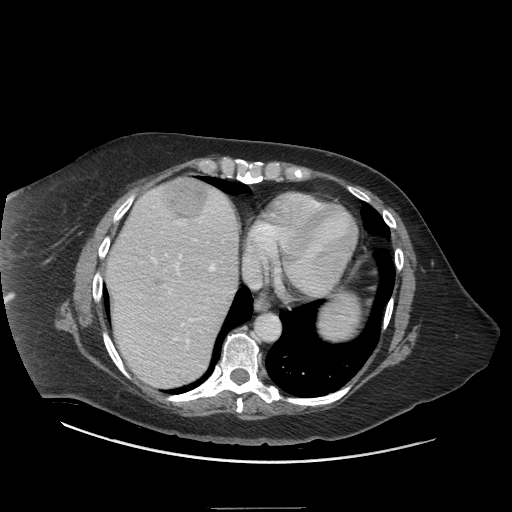
Contrast-enhanced abdominal CT (liver protocol), one axial slice; slice 60 of 81 in the series (ordered by position); soft-tissue window (W 400 / L 40 HU); 512 × 512 image matrix. From the clinical record (not read from this slice): diagnosis: hepatocellular carcinoma (patient treated with transarterial chemoembolisation; whether this scan precedes or follows treatment is not stated here); TNM stage (as recorded): Stage-II; Child-Pugh class: A; tumour nodularity: multinodular; tumour size: 1.7 cm.
Outlined on this slice (semi-automatic segmentation, software-assisted and operator-edited):
- abdominal aorta: bounding box <256,314,279,341> (left, top, right, bottom; pixels)
- liver parenchyma outside the tumour (the mass and vessels are separate outlines, so this box may not span the whole liver): <106,178,238,388>
- mass: <142,180,211,309>
- liver vessels: <116,192,224,372>